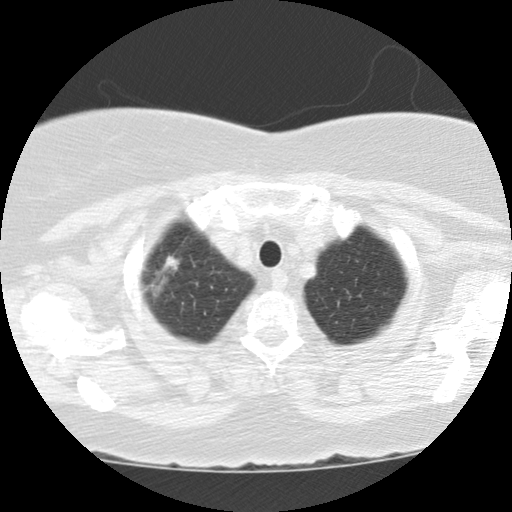
Low-dose screening chest CT, axial slice, baseline screening round, lung window (W 1500 / L -600 HU), slice 10 of 112 in the series. Female, age 67 years at enrolment.
• Expert reader's lesion annotation, bounding box <134,240,198,305> (left, top, right, bottom; pixels).
• The screening reader recorded 3 non-calcified nodules or masses ≥4 mm on this exam (right upper lobe, right lower lobe, right upper lobe); which of them this box marks is not recorded.
• Official screen result: positive, change unspecified: nodule(s) >= 4 mm or enlarging nodule(s), mass(es), or other non-specific abnormalities suspicious for lung cancer.